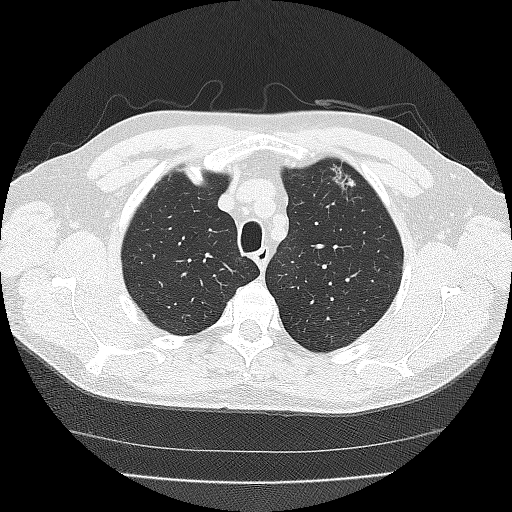
Low-dose screening chest CT, one axial slice. Slice 132 of 167 in the series (ordered by position). Reconstruction kernel FC30. 120 kVp. Lung window (W 1500 / L -600 HU). 2 mm slice thickness. 512 × 512 image matrix.
Annotated regions visible in this slice (expert manual segmentation):
- lesion 1 (tumor, upper lobe of left lung): bounding box [x1, y1, x2, y2] px = [331, 162, 356, 190]